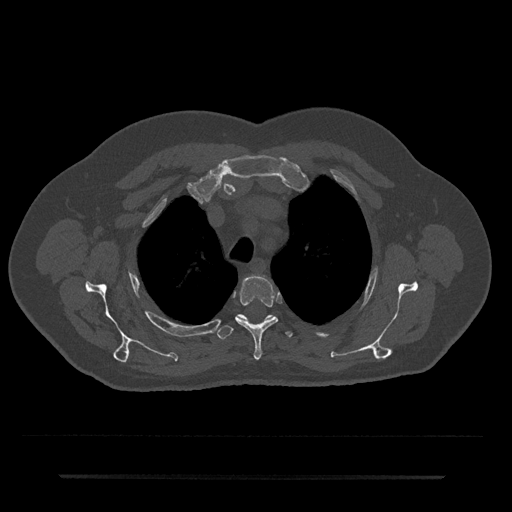
CT including the spine, one axial slice. Position 559 of 797 along the scan axis. Reconstruction kernel Br40s/3. 120 kVp. Bone window (W 1800 / L 400 HU). 0.5 mm slice thickness. 512 × 512 image matrix. Male patient, age 69 years. Case-level facts recorded for this patient, not image findings: primary cancer: prostate.
Outlined on this slice (semi-automatically segmented with operator editing):
- T3 vertebra: bounding box <235,276,278,360> (left, top, right, bottom; pixels)
- T4 vertebra: <217,314,293,340>